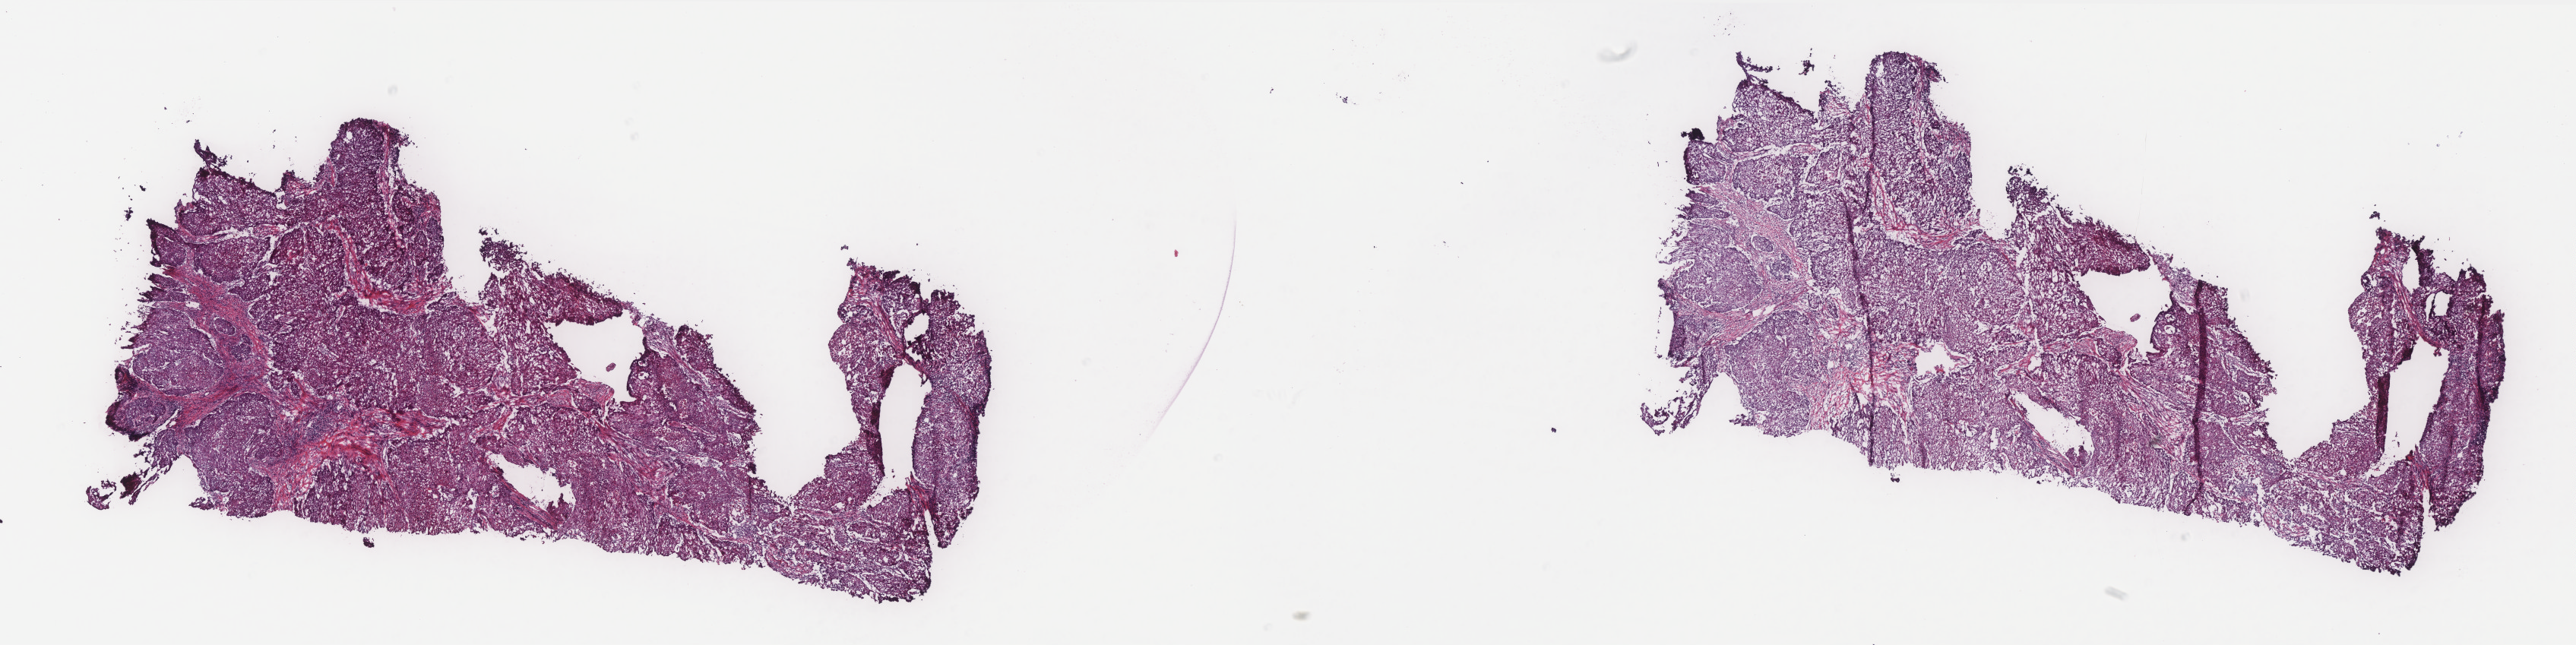
Digitized H&E-stained tissue section (whole slide), whole scanned area (about 27.2 x 6.8 mm, from a 40x scan) shown as a low-resolution overview; frozen section from the bottom of the tissue portion; sample: primary tumour, bladder. Female, age 70 years at initial diagnosis. Histologic grade: high grade. Pathologist review of this section (percent, as recorded): tumour cells 60%, tumour nuclei 70%, normal cells 0%, stromal cells 30%, necrosis 10%. Infiltration values recorded for this section: lymphocyte infiltration 10%, monocyte infiltration 0%, neutrophil infiltration 5%.
AJCC pathologic stage: III (6th edition). Histologic diagnosis: Transitional cell carcinoma.